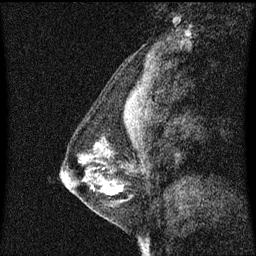
Breast MRI (dynamic contrast-enhanced), one sagittal slice; position 20 of 60 along the scan axis; dynamic contrast-enhanced series, image 2 of 3 at this slice position (ordered by acquisition); 1.5 T; TE 4.2 ms, TR 8.4 ms; 256 × 256 image matrix, field of view 200 × 200 mm. Patient: female, 41 years. From the clinical record (not read from this slice): setting: breast cancer imaged before/during neoadjuvant chemotherapy; receptor status: triple-negative.
Structures marked on this image (semi-automatic segmentation, software-assisted and operator-edited):
- analysis volume of interest (the breast-tissue region the enhancement analysis was run in; not a lesion): box from (x=64, y=132) to (x=133, y=209) px
- tumour enhancement mask (voxels above the 70 % enhancement threshold inside the analysis volume of interest): (x=104, y=188)–(x=117, y=195)